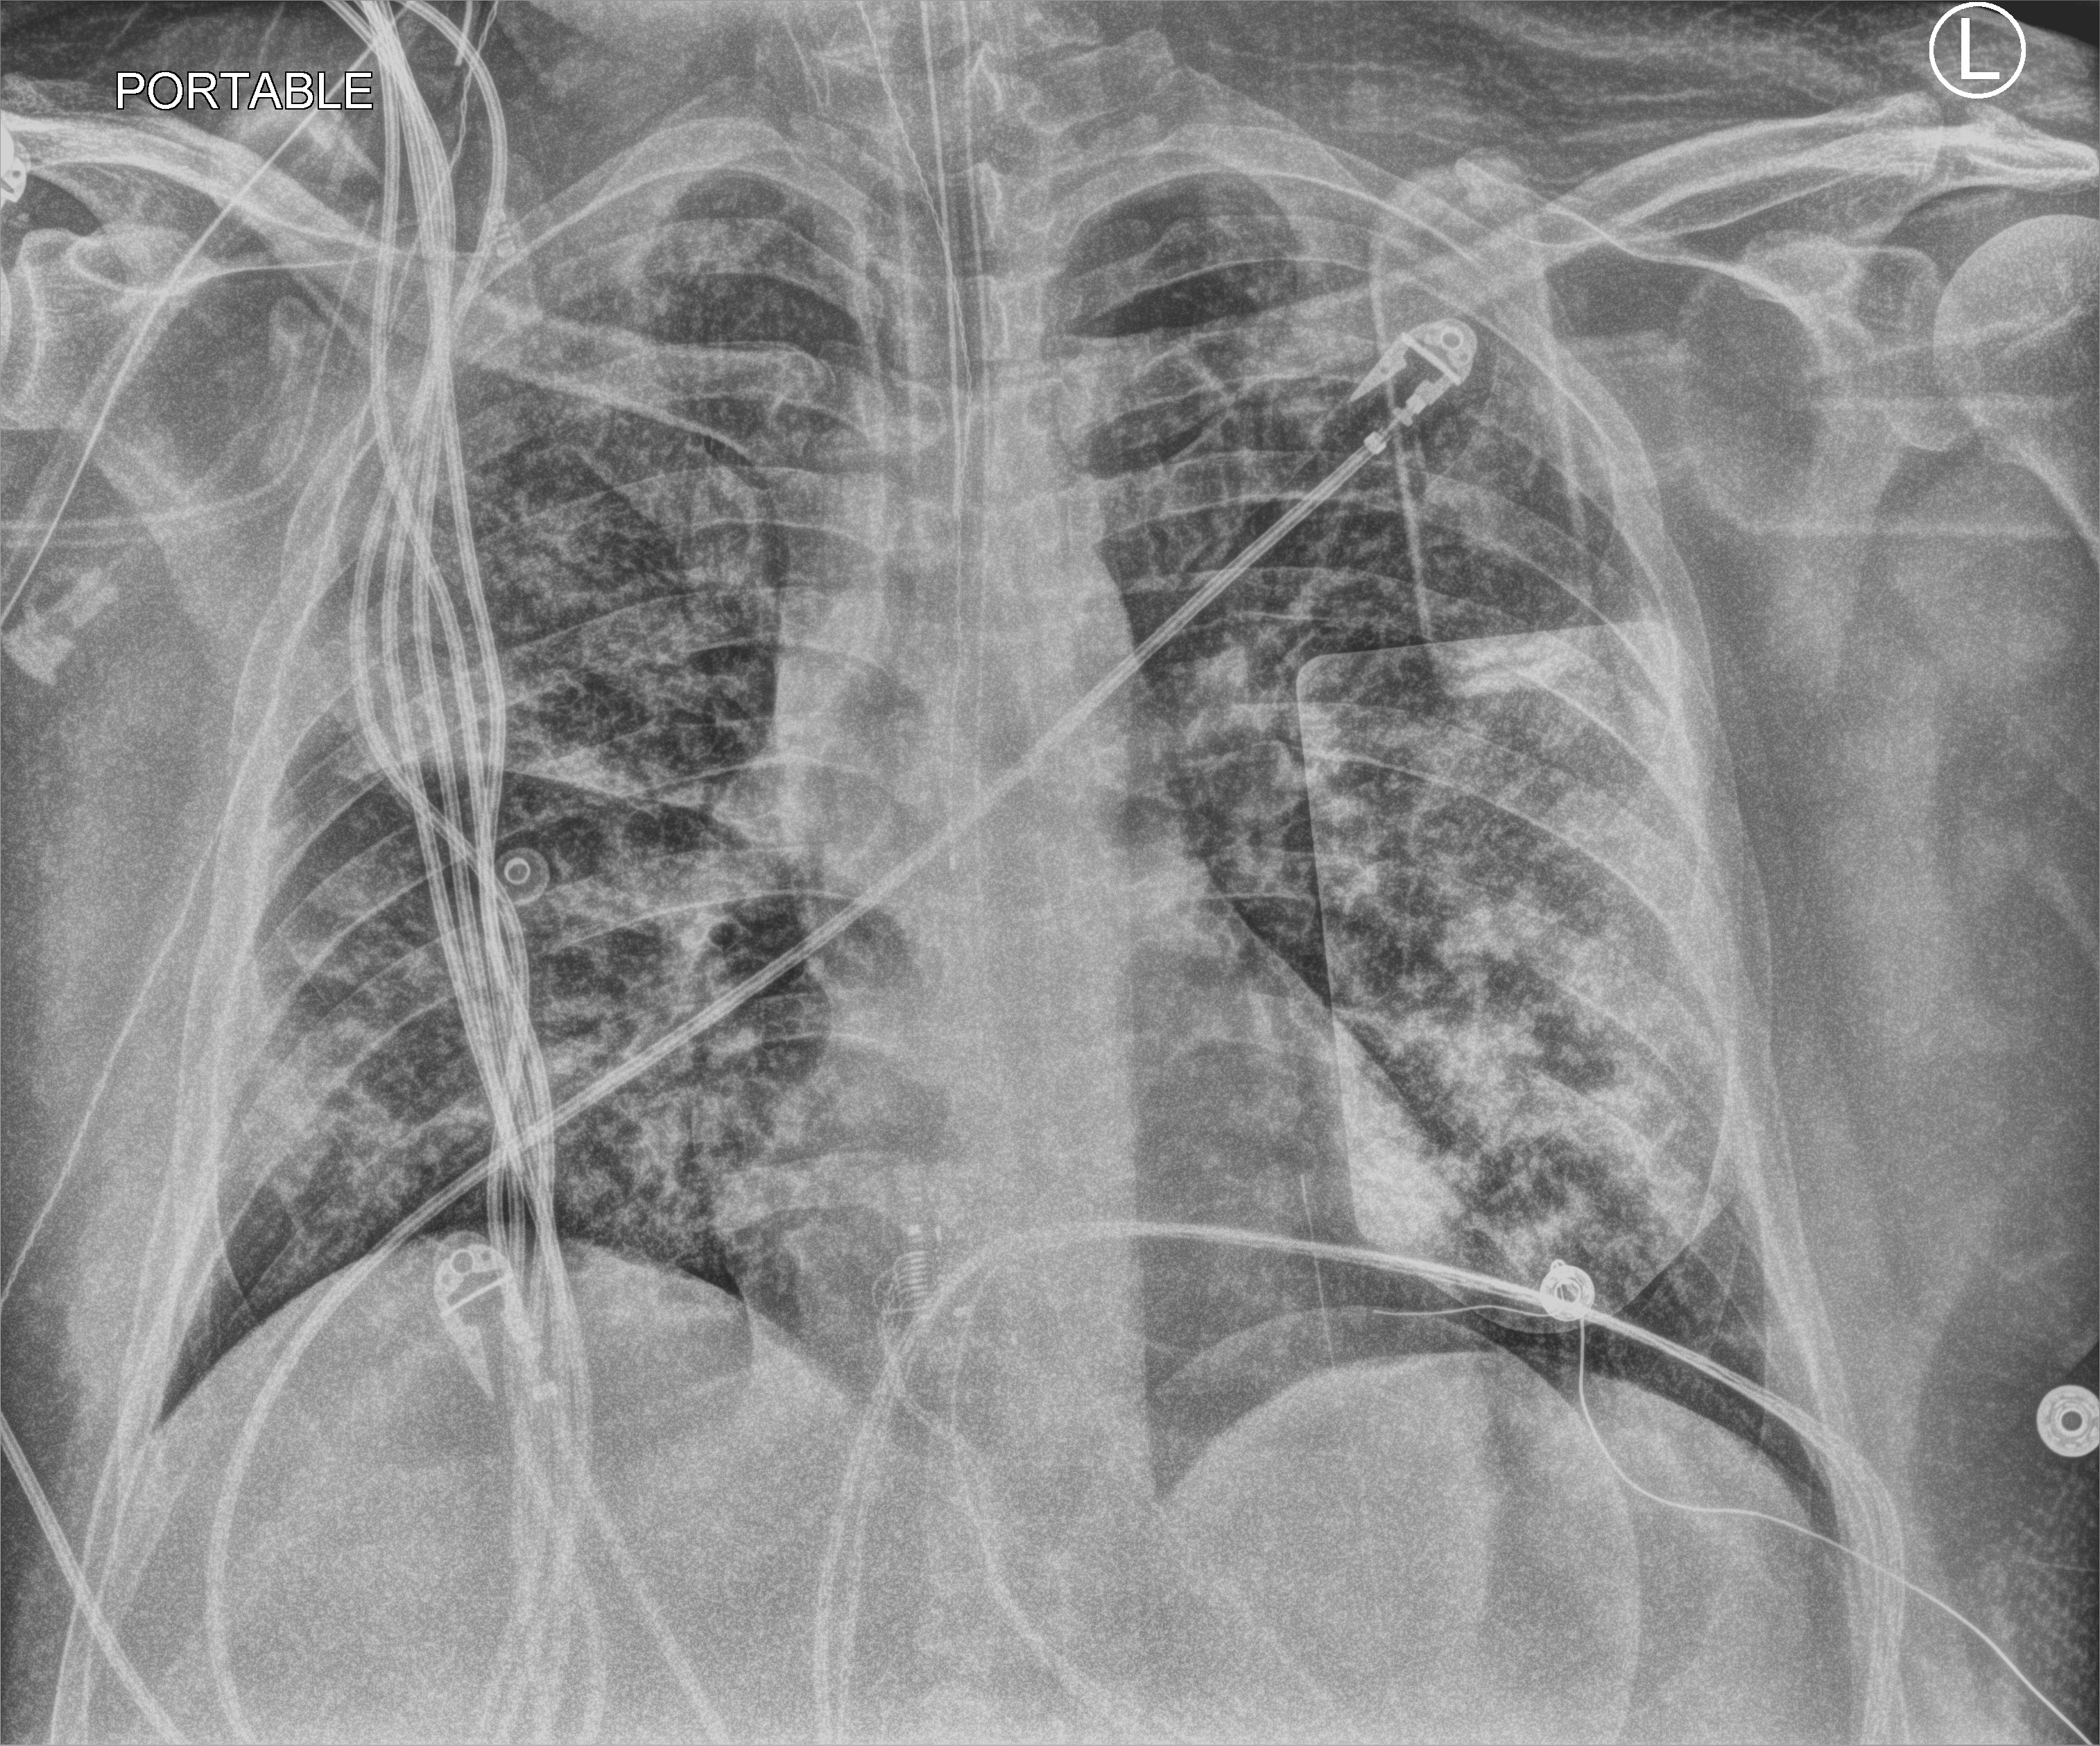
Bedside chest radiograph (computed radiography); anteroposterior (AP) projection. Patient hospitalised with COVID-19, aged 18–59 years.
Hospital-stay facts (about this admission, not read from this image; timing relative to this image not recorded): admitted to intensive care during this hospital stay: yes.